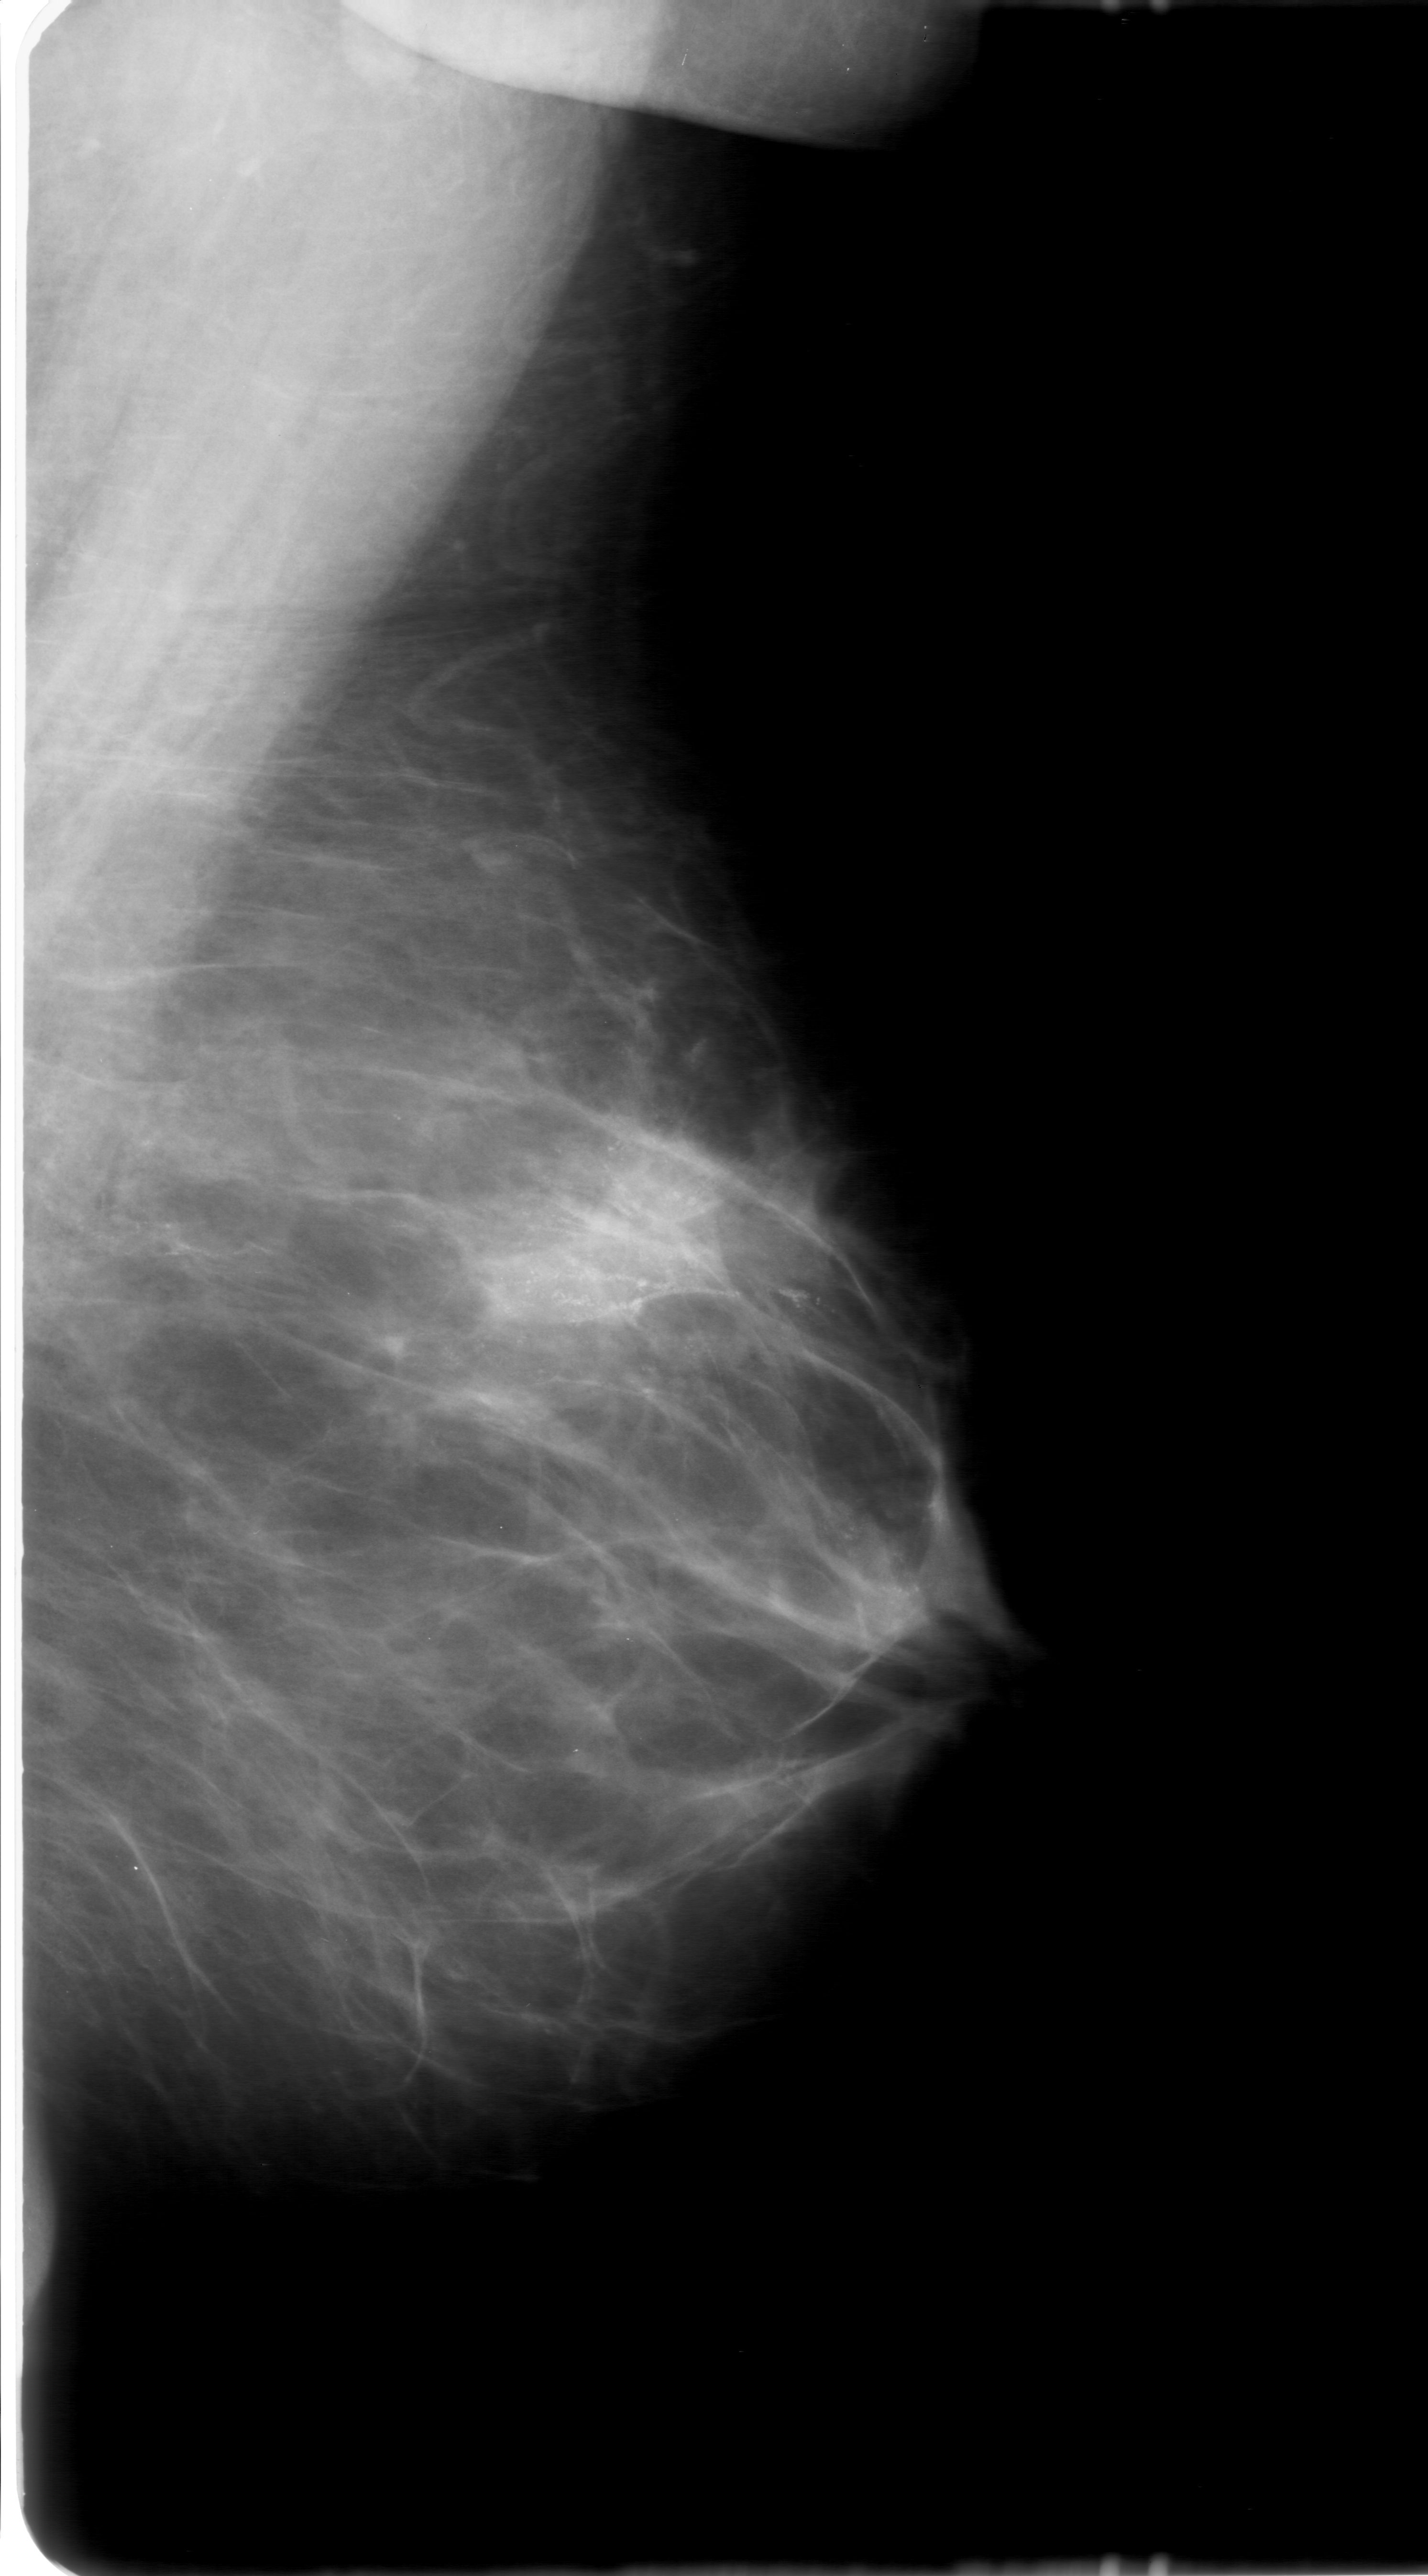
Scanned film-screen mammogram; left breast; MLO view; BI-RADS breast density category 2 (scale 1–4).
- Marked findings (only marked abnormalities are described; nothing is implied about the rest of the image): calcifications, morphology amorphous, distribution linear; BI-RADS assessment category 5; pathology (as recorded): malignant.